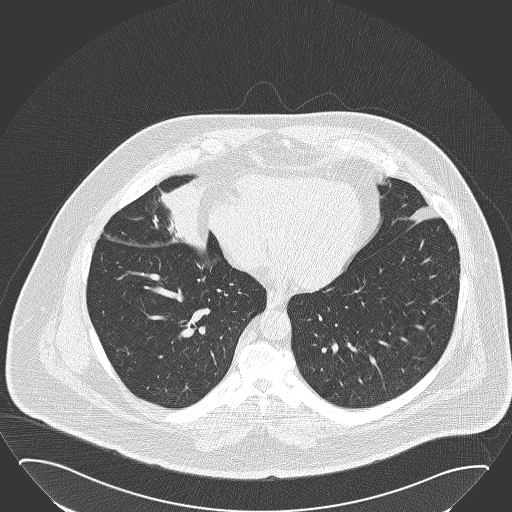
Low-dose screening chest CT, one axial slice; slice 62 of 168 in the series (ordered by position); lung window (W 1500 / L -600 HU); 2 mm slice thickness; 512 × 512 image matrix.
Annotated regions visible in this slice (manually delineated by an expert):
- lesion 1 (tumor, hilum of right lung): bounding box (x1, y1, x2, y2) in pixels: (159, 177, 207, 252)